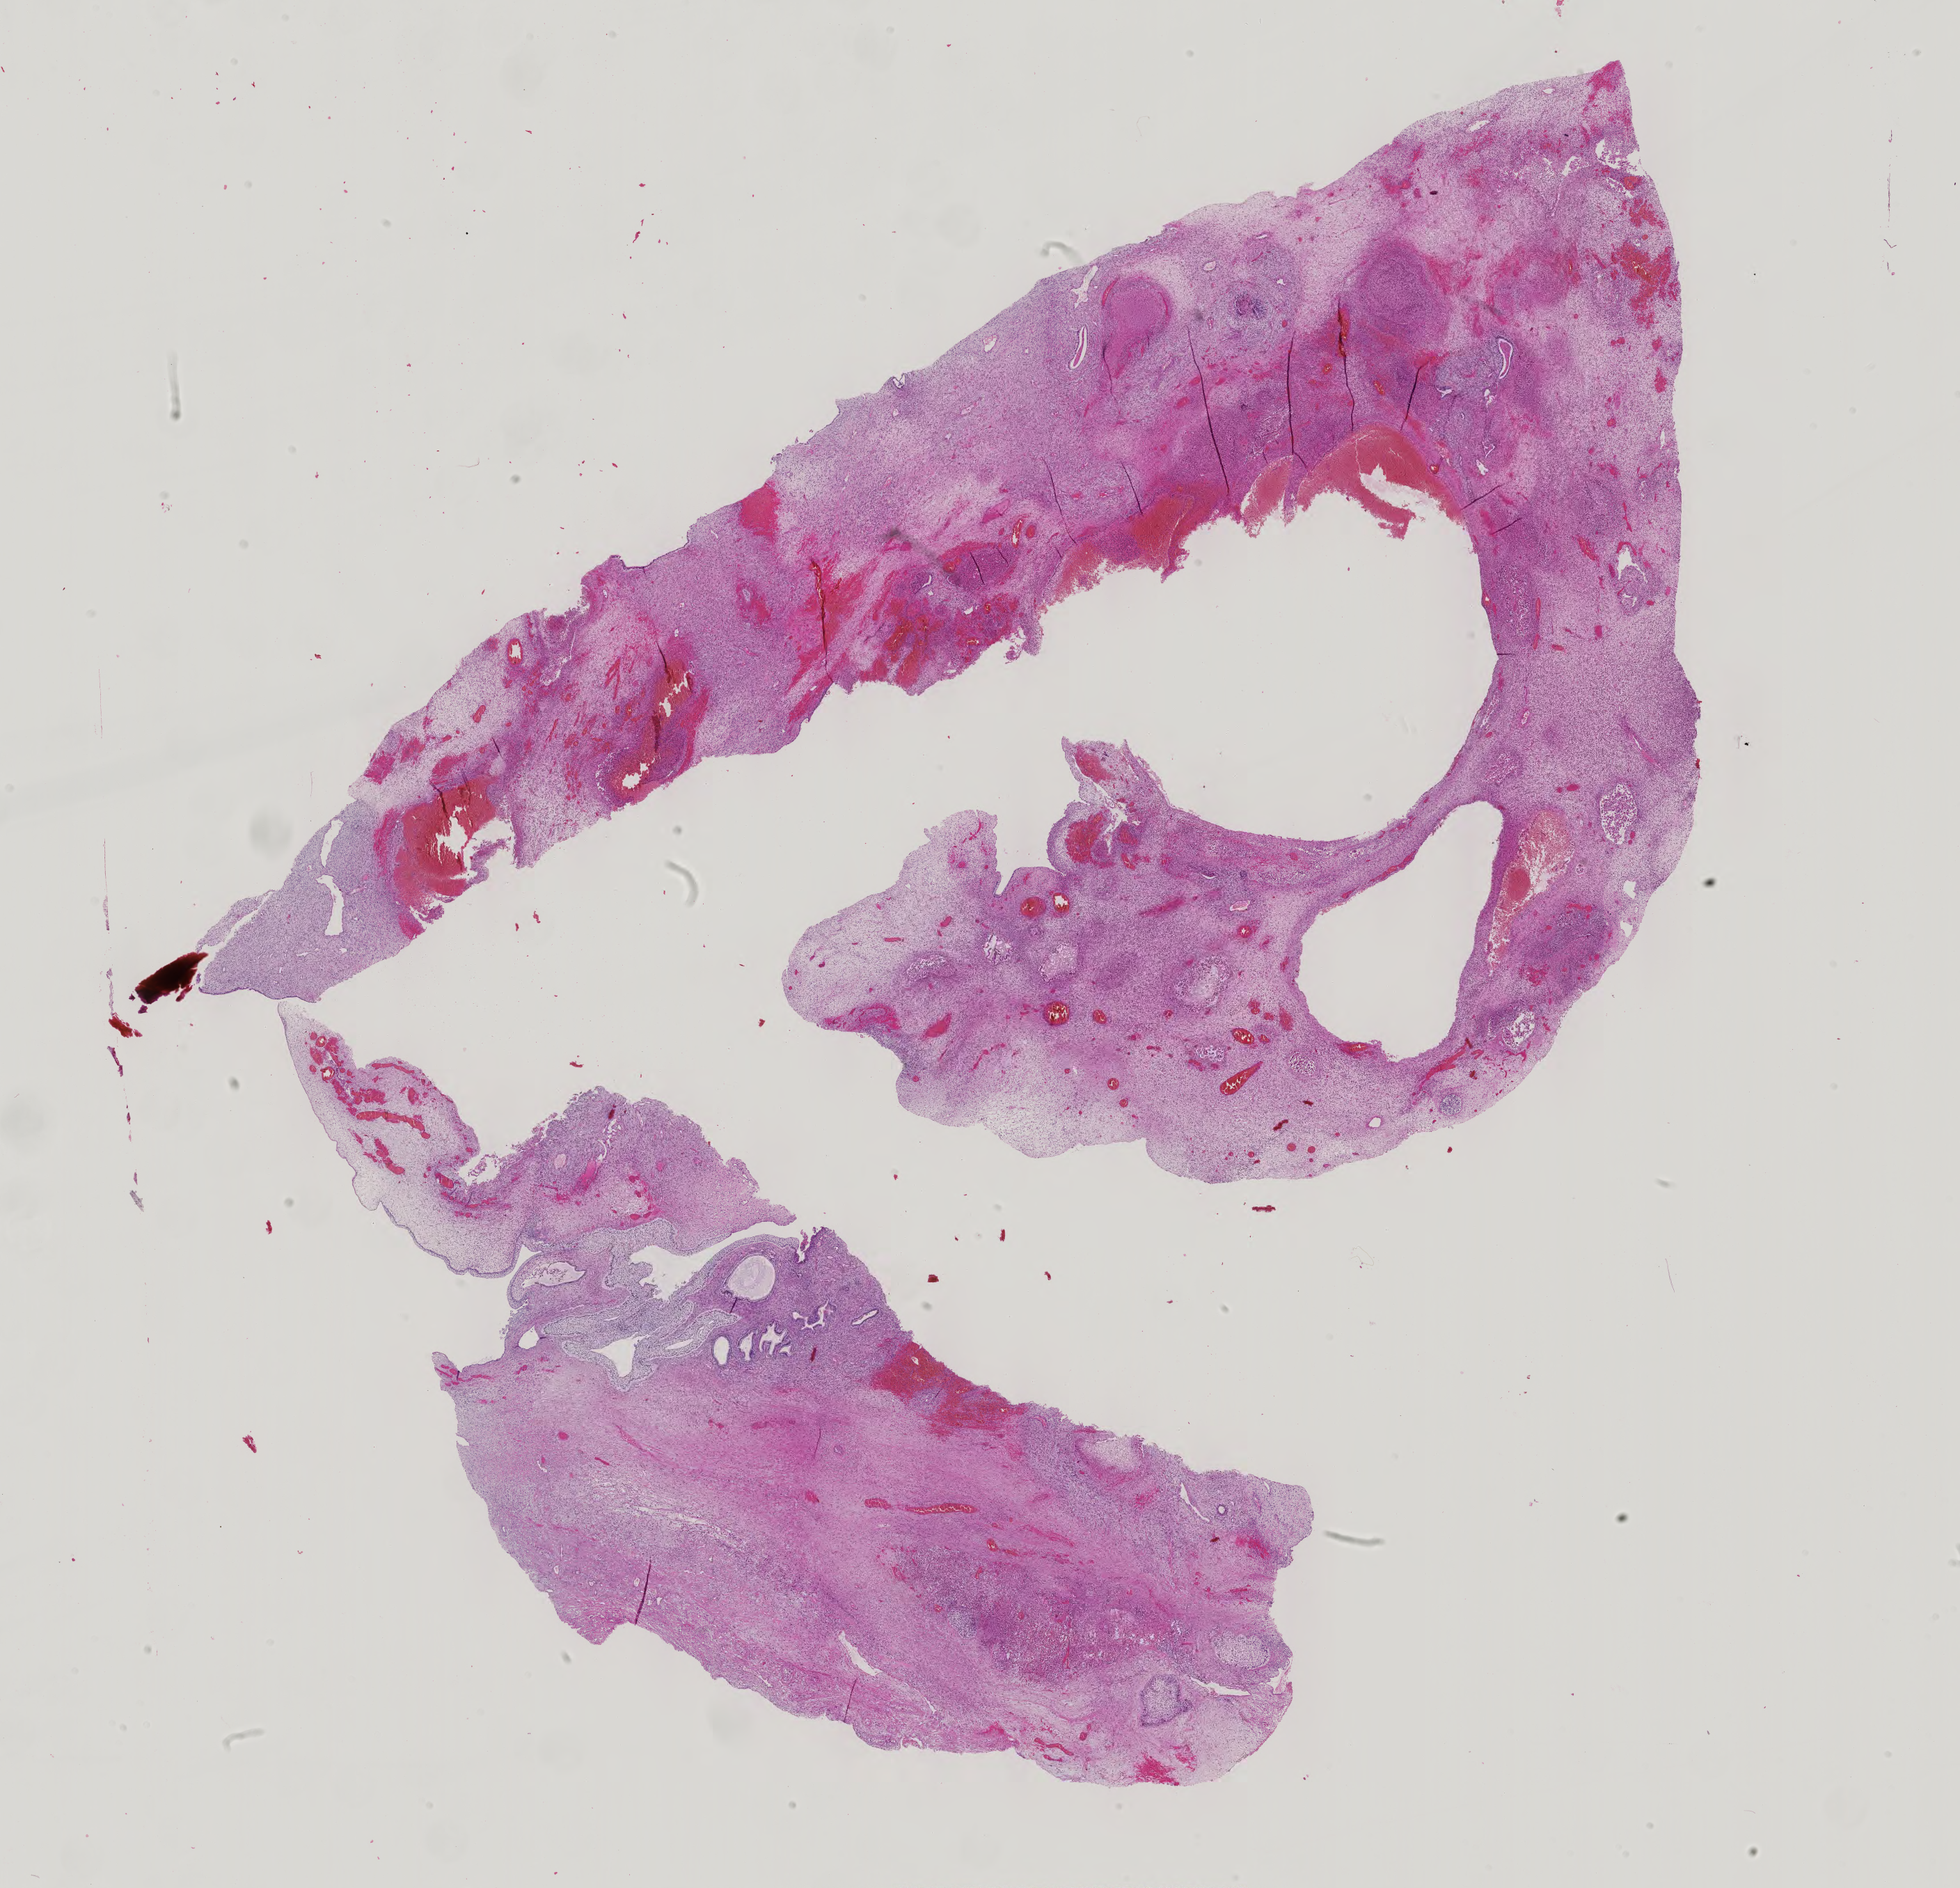
H&E whole-slide image — a low-resolution overview of the entire scanned area, about 20.5 x 19.8 mm (slide scanned at 40x). Male patient.
Specimen: FFPE section; primary tumour sample from the testis.